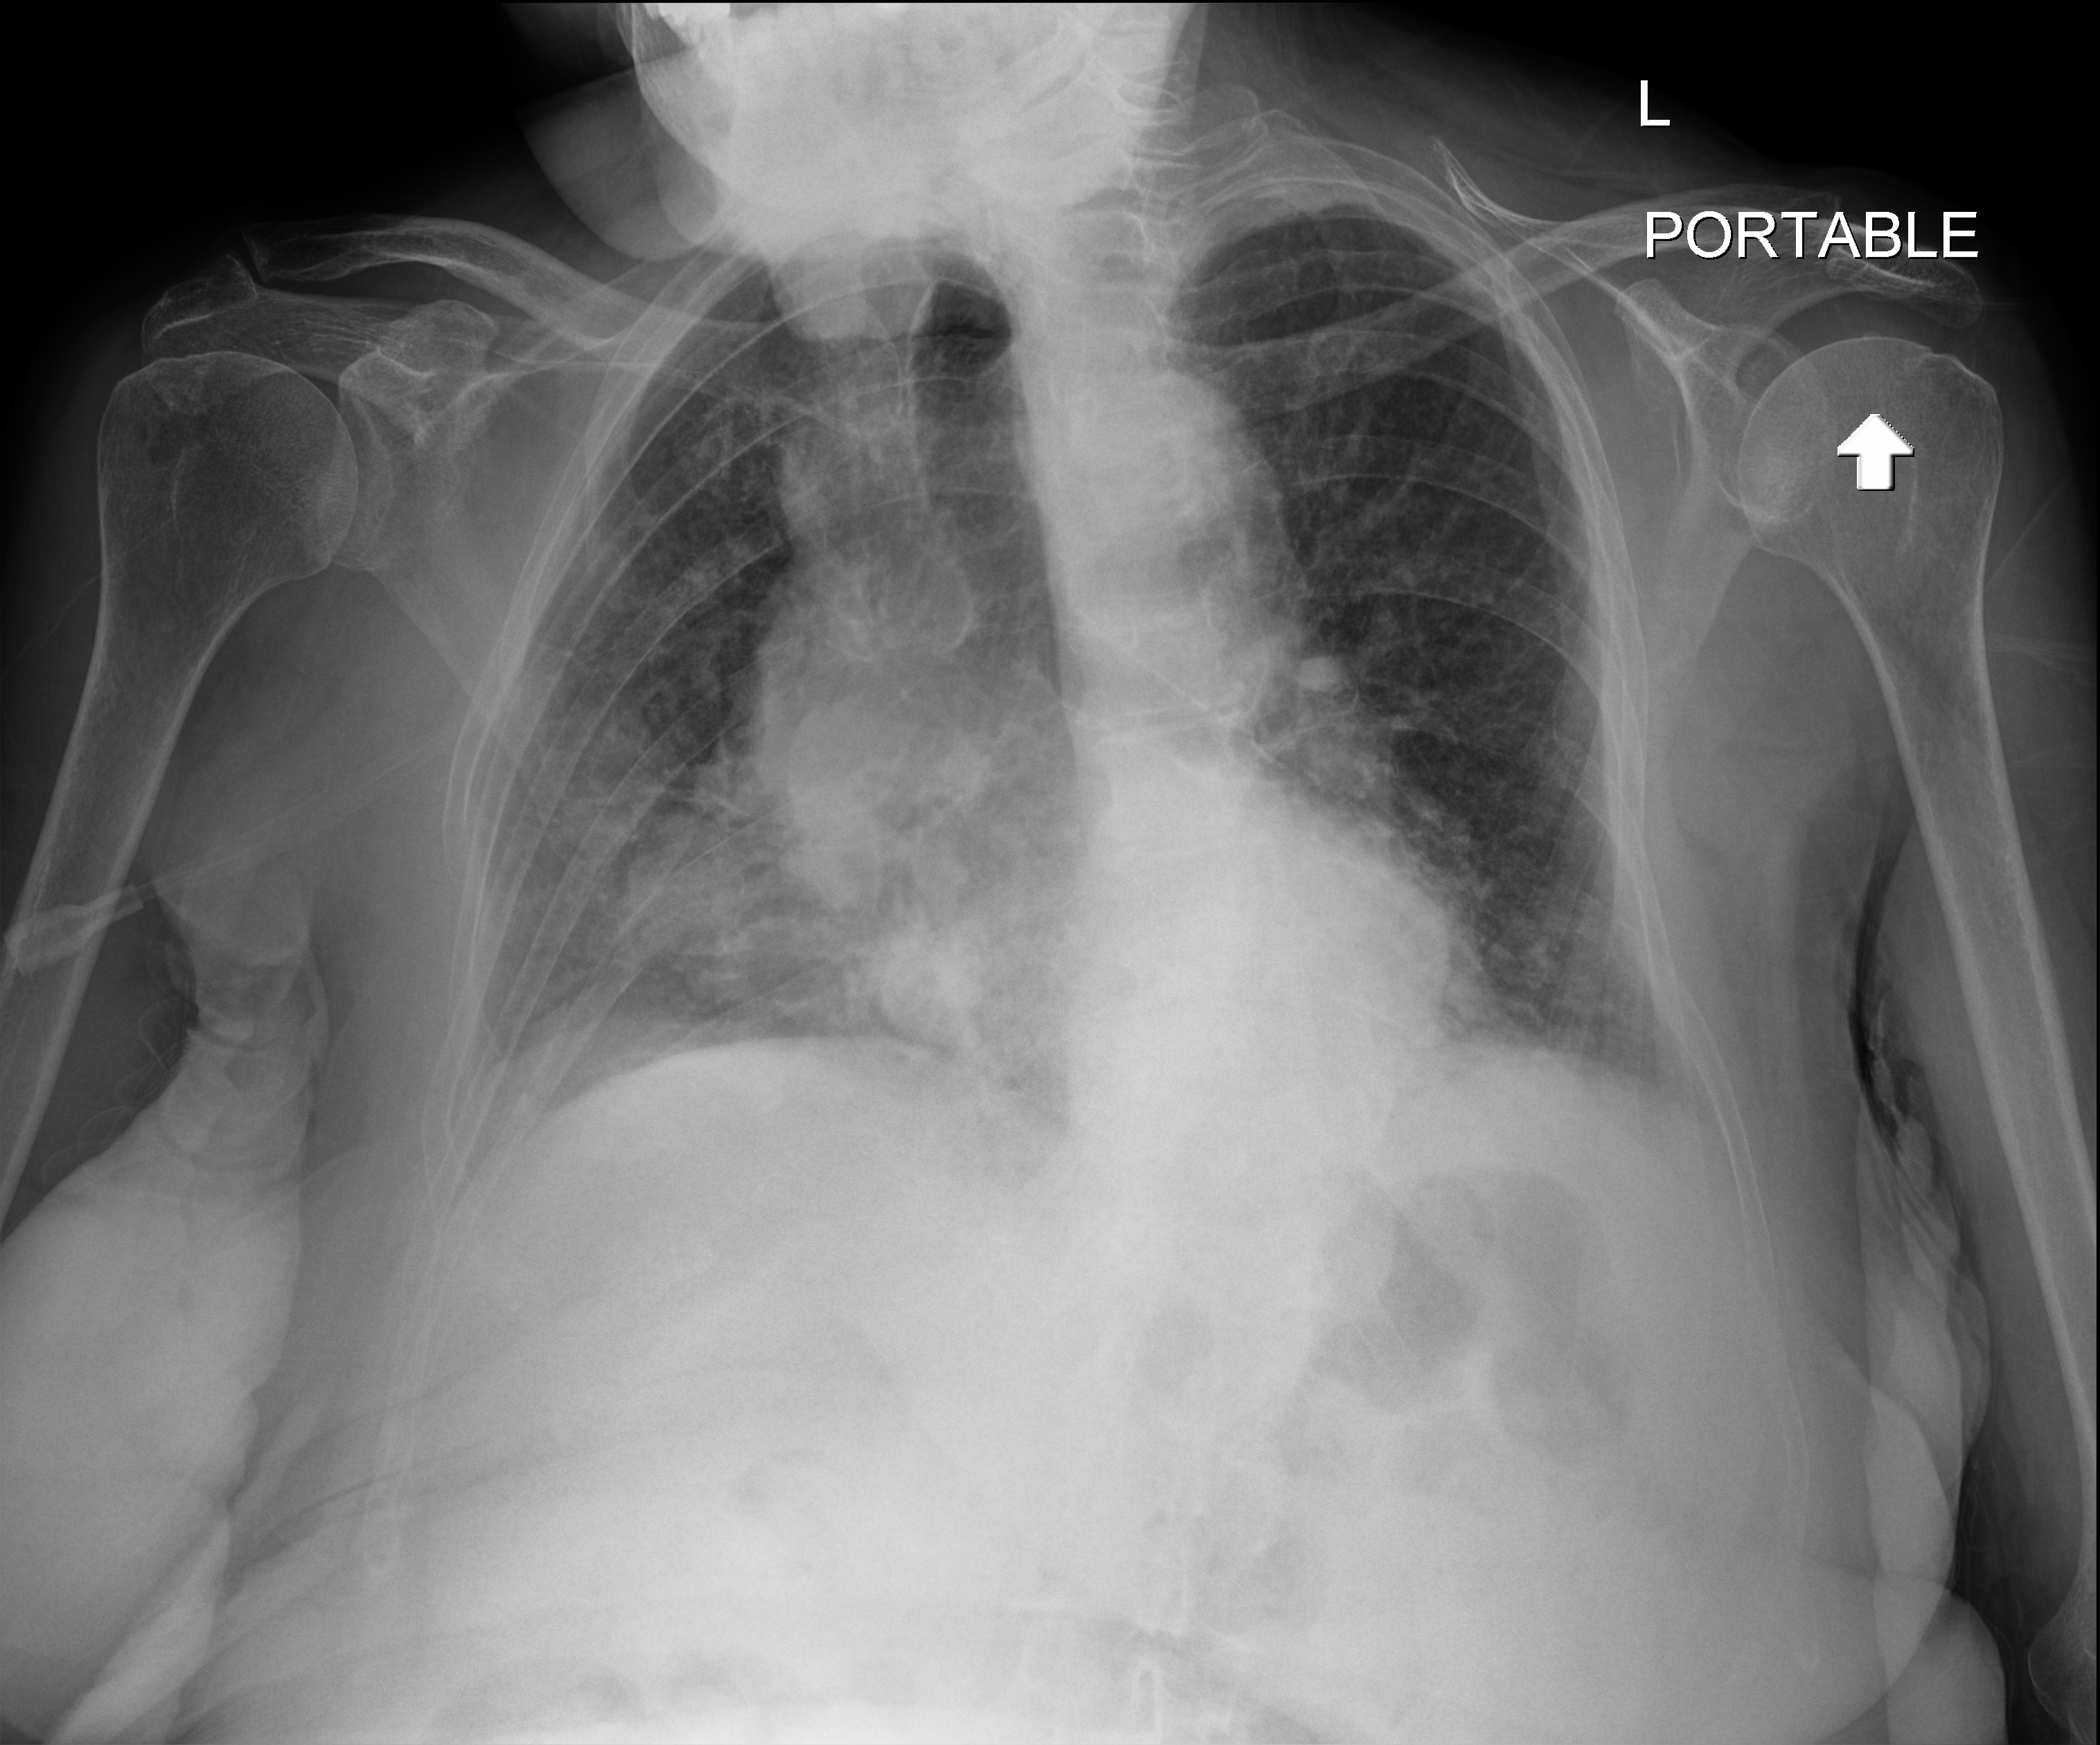
Chest radiograph (digital radiography); anteroposterior (AP) projection. Female patient hospitalised with COVID-19, age 75–90 years.
From the hospital-stay record, not from the radiograph (when in the stay this image was taken is not recorded): mechanically ventilated during this hospital stay: no.